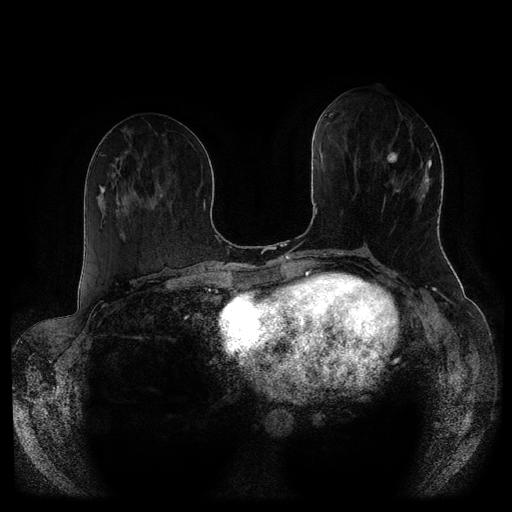
Breast MRI (dynamic contrast-enhanced, multi-phase), one axial slice. Position 42 of 116 along the scan axis. Dynamic contrast-enhanced series, time point 2 of 5 at this slice position (early post-contrast). 1.5 T. TE 2.6 ms, TR 5.3 ms. 512 × 512 image matrix. Female patient, age 51 years.
Structures marked on this image (semi-automatically segmented with operator editing):
- breast lesion (labelled 'tumour' in the annotation; benign lesions carry a separate 'benign' label): bounding box <387,152,400,193> (left, top, right, bottom; pixels)